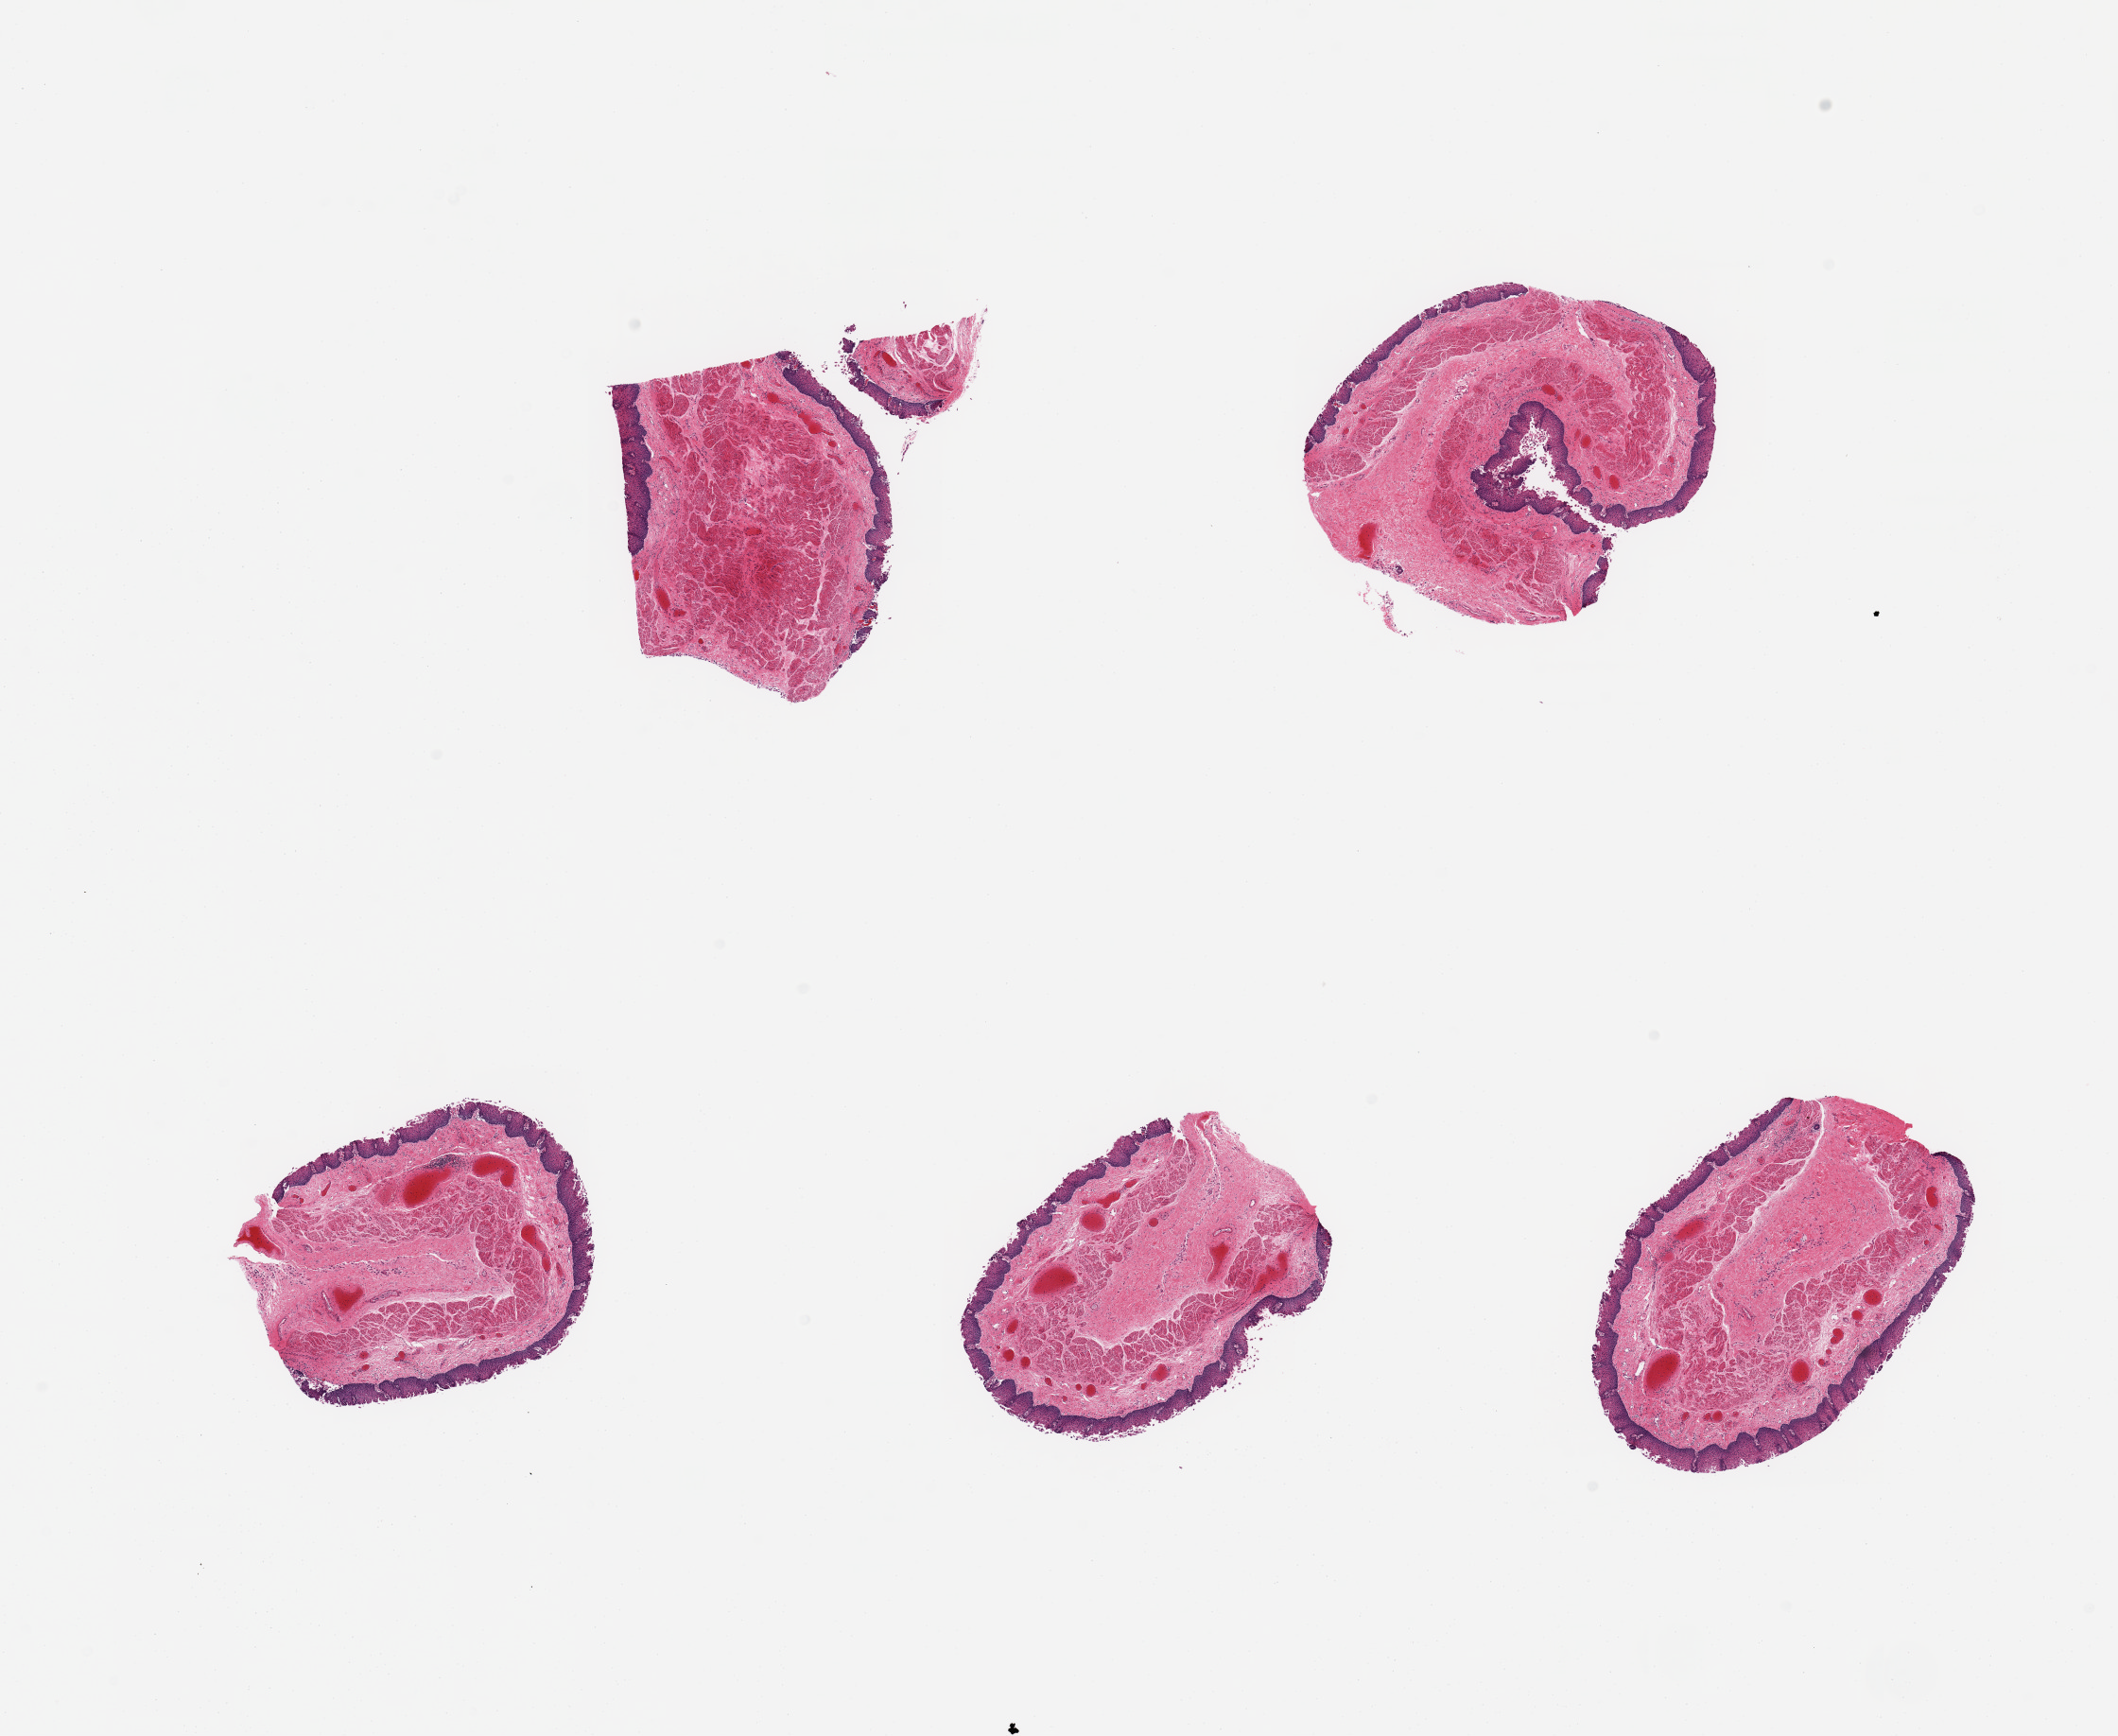
Whole-slide image, haematoxylin and eosin stain — whole scanned area (about 17.7 x 14.5 mm, acquisition: 20x scan) shown as a low-resolution overview; PAXgene-fixed, paraffin-embedded tissue; target tissue: esophageal mucous membrane; tissue donor sample. Donor sex: female.
Reviewer comment on this tissue sample: 5 pieces; partly disrupted squamous epithelium.